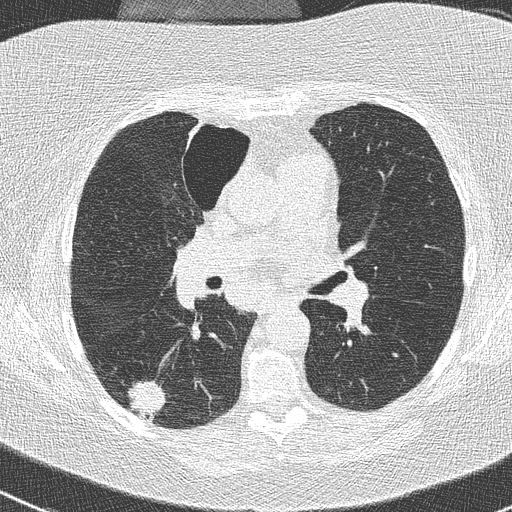
Low-dose screening chest CT, axial slice. Baseline screening round. Lung window (W 1500 / L -600 HU). 2 mm slice thickness. Lung (sharp) reconstruction kernel (B50f). Slice 116 of 261 in the series. 512 × 512 image matrix, field of view 310 × 310 mm. Female, age 74 years at enrolment. Former smoker at enrolment.
Lesion marked by an expert reader, bounding box [x1, y1, x2, y2] px = [119, 375, 174, 428]. The screening reader recorded 3 non-calcified nodules or masses ≥4 mm on this exam (right lower lobe, right upper lobe, left lower lobe); which of them this box marks is not recorded. Official screen result: positive, change unspecified: nodule(s) >= 4 mm or enlarging nodule(s), mass(es), or other non-specific abnormalities suspicious for lung cancer. Later outcome: lung cancer diagnosed 16 days after this screen — non-small cell carcinoma, right lower lobe, poorly differentiated (G3), stage IIIA (AJCC 6th edition), 28 mm at pathology.